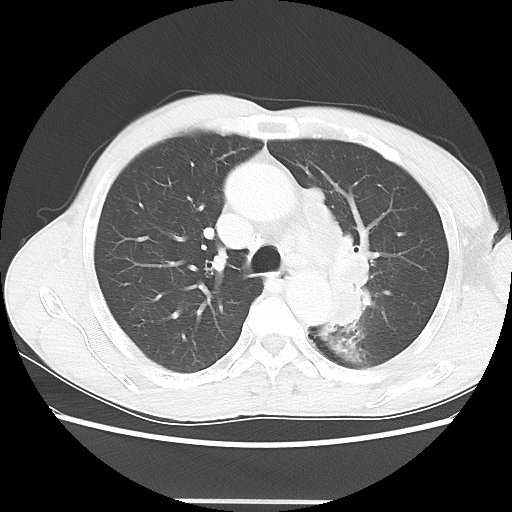
Chest CT, one axial slice; position 44 of 62 along the scan axis; reconstruction kernel LUNG; lung window (W 1500 / L -600 HU); 5 mm slice thickness; 512 × 512 image matrix, field of view 360 × 360 mm. Male patient, age 61 years. From the clinical record (not read from this slice): clinical TNM (as recorded): T3 N1 M1.
Outlined on this slice (bounding box drawn by a radiologist):
- lung tumour (recorded histology: adenocarcinoma): bounding box <295,174,371,339> (left, top, right, bottom; pixels)